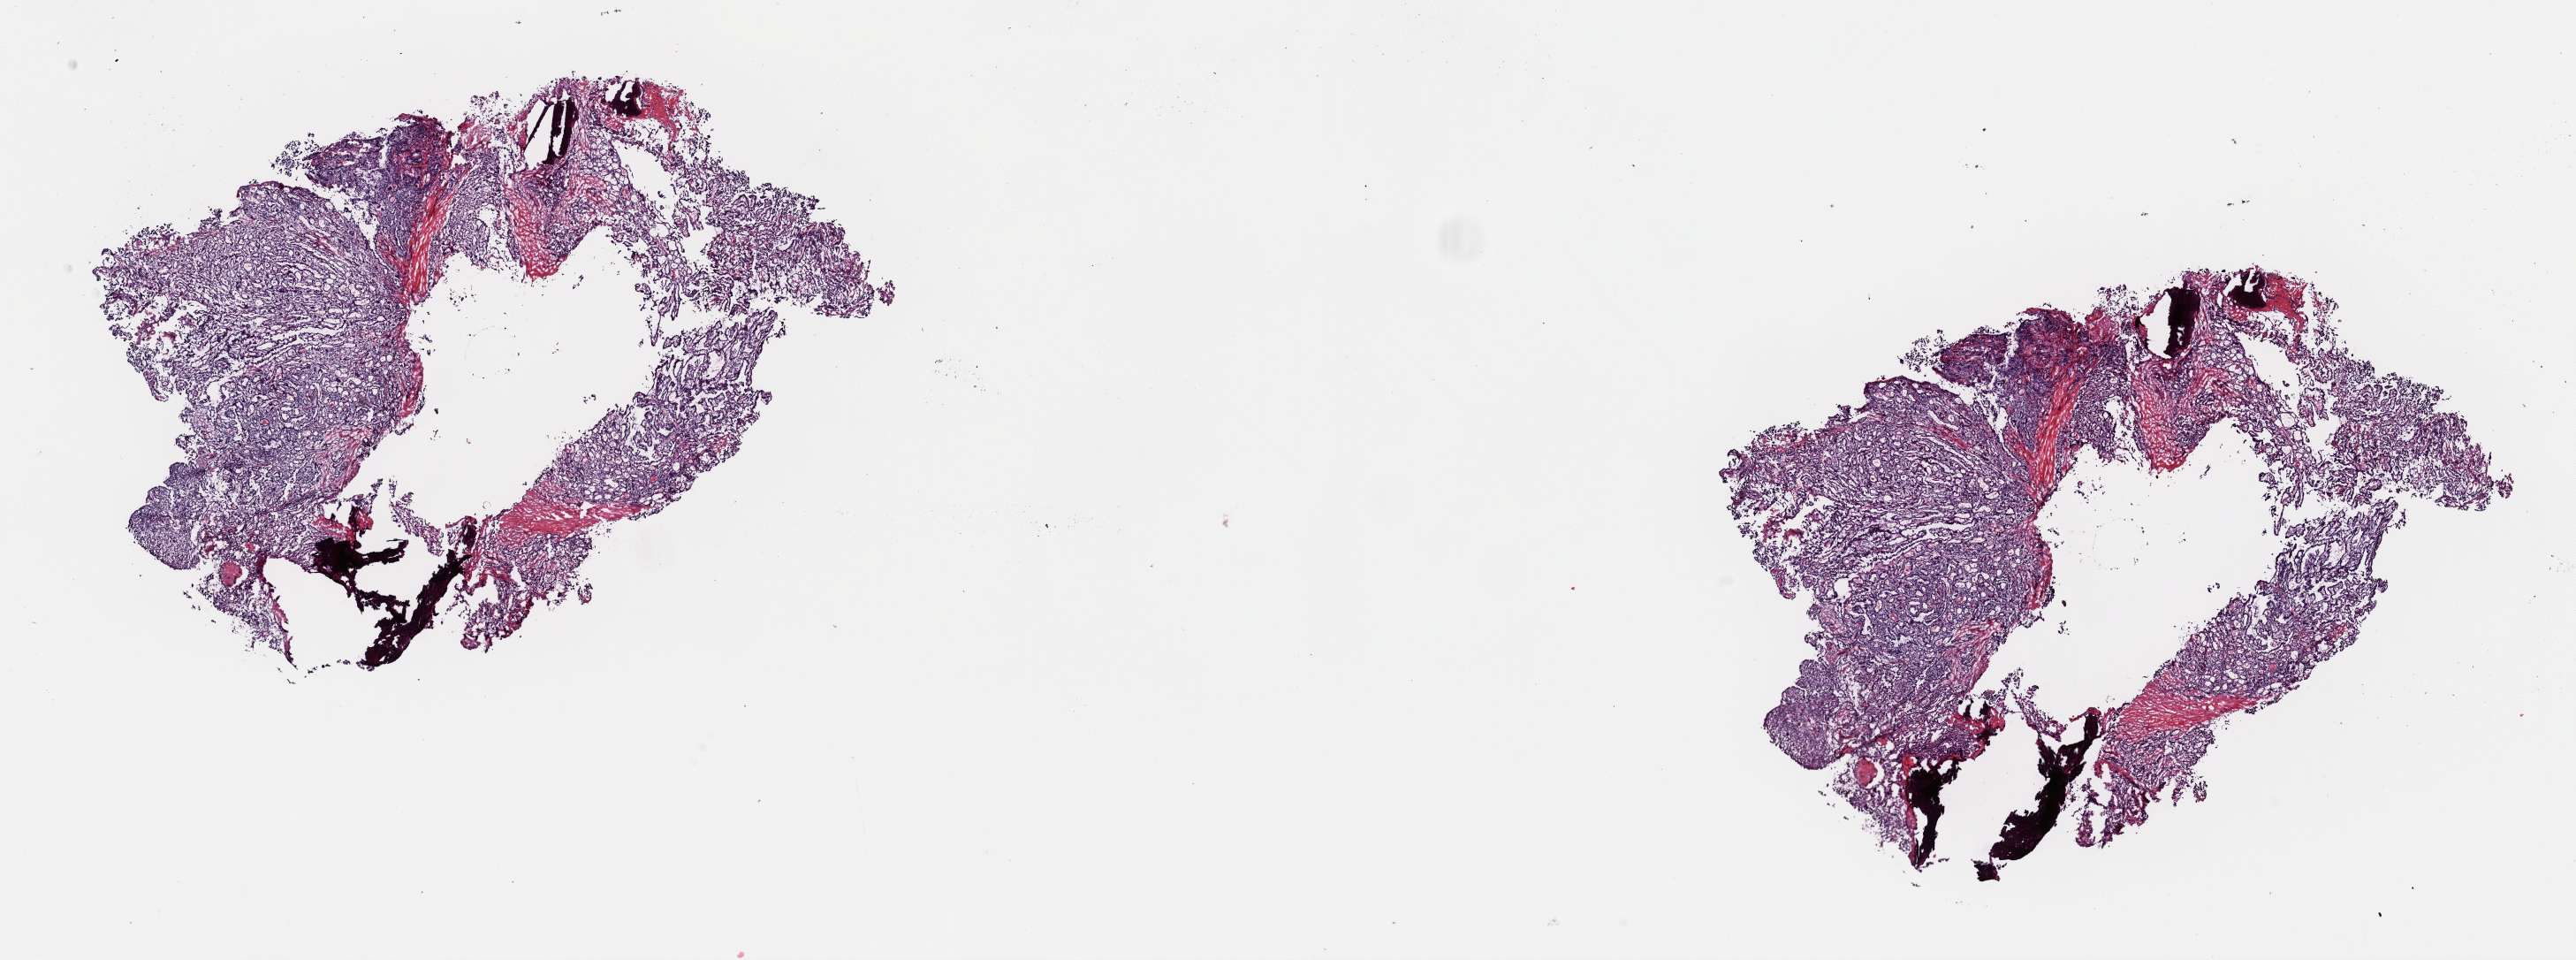
Digitized H&E tissue section (whole slide), shown as a low-resolution overview of the whole scanned area (about 23.0 x 8.6 mm), frozen section from the top of the tissue portion, thyroid, primary tumour sample. Female, age 34 years at initial diagnosis. Slide review estimates, as recorded: tumour cells 80%, tumour nuclei 80%, normal cells 0%, stromal cells 20%, necrosis 0%. Inflammatory infiltration, as recorded: lymphocyte infiltration 2%, monocyte infiltration 0%, neutrophil infiltration 0%.
• TNM: T1b N1a M0
• lymph nodes positive (case pathology): 2 of 3 examined
• AJCC pathologic stage: I
• pathologic diagnosis: Papillary adenocarcinoma, NOS (thyroid gland)